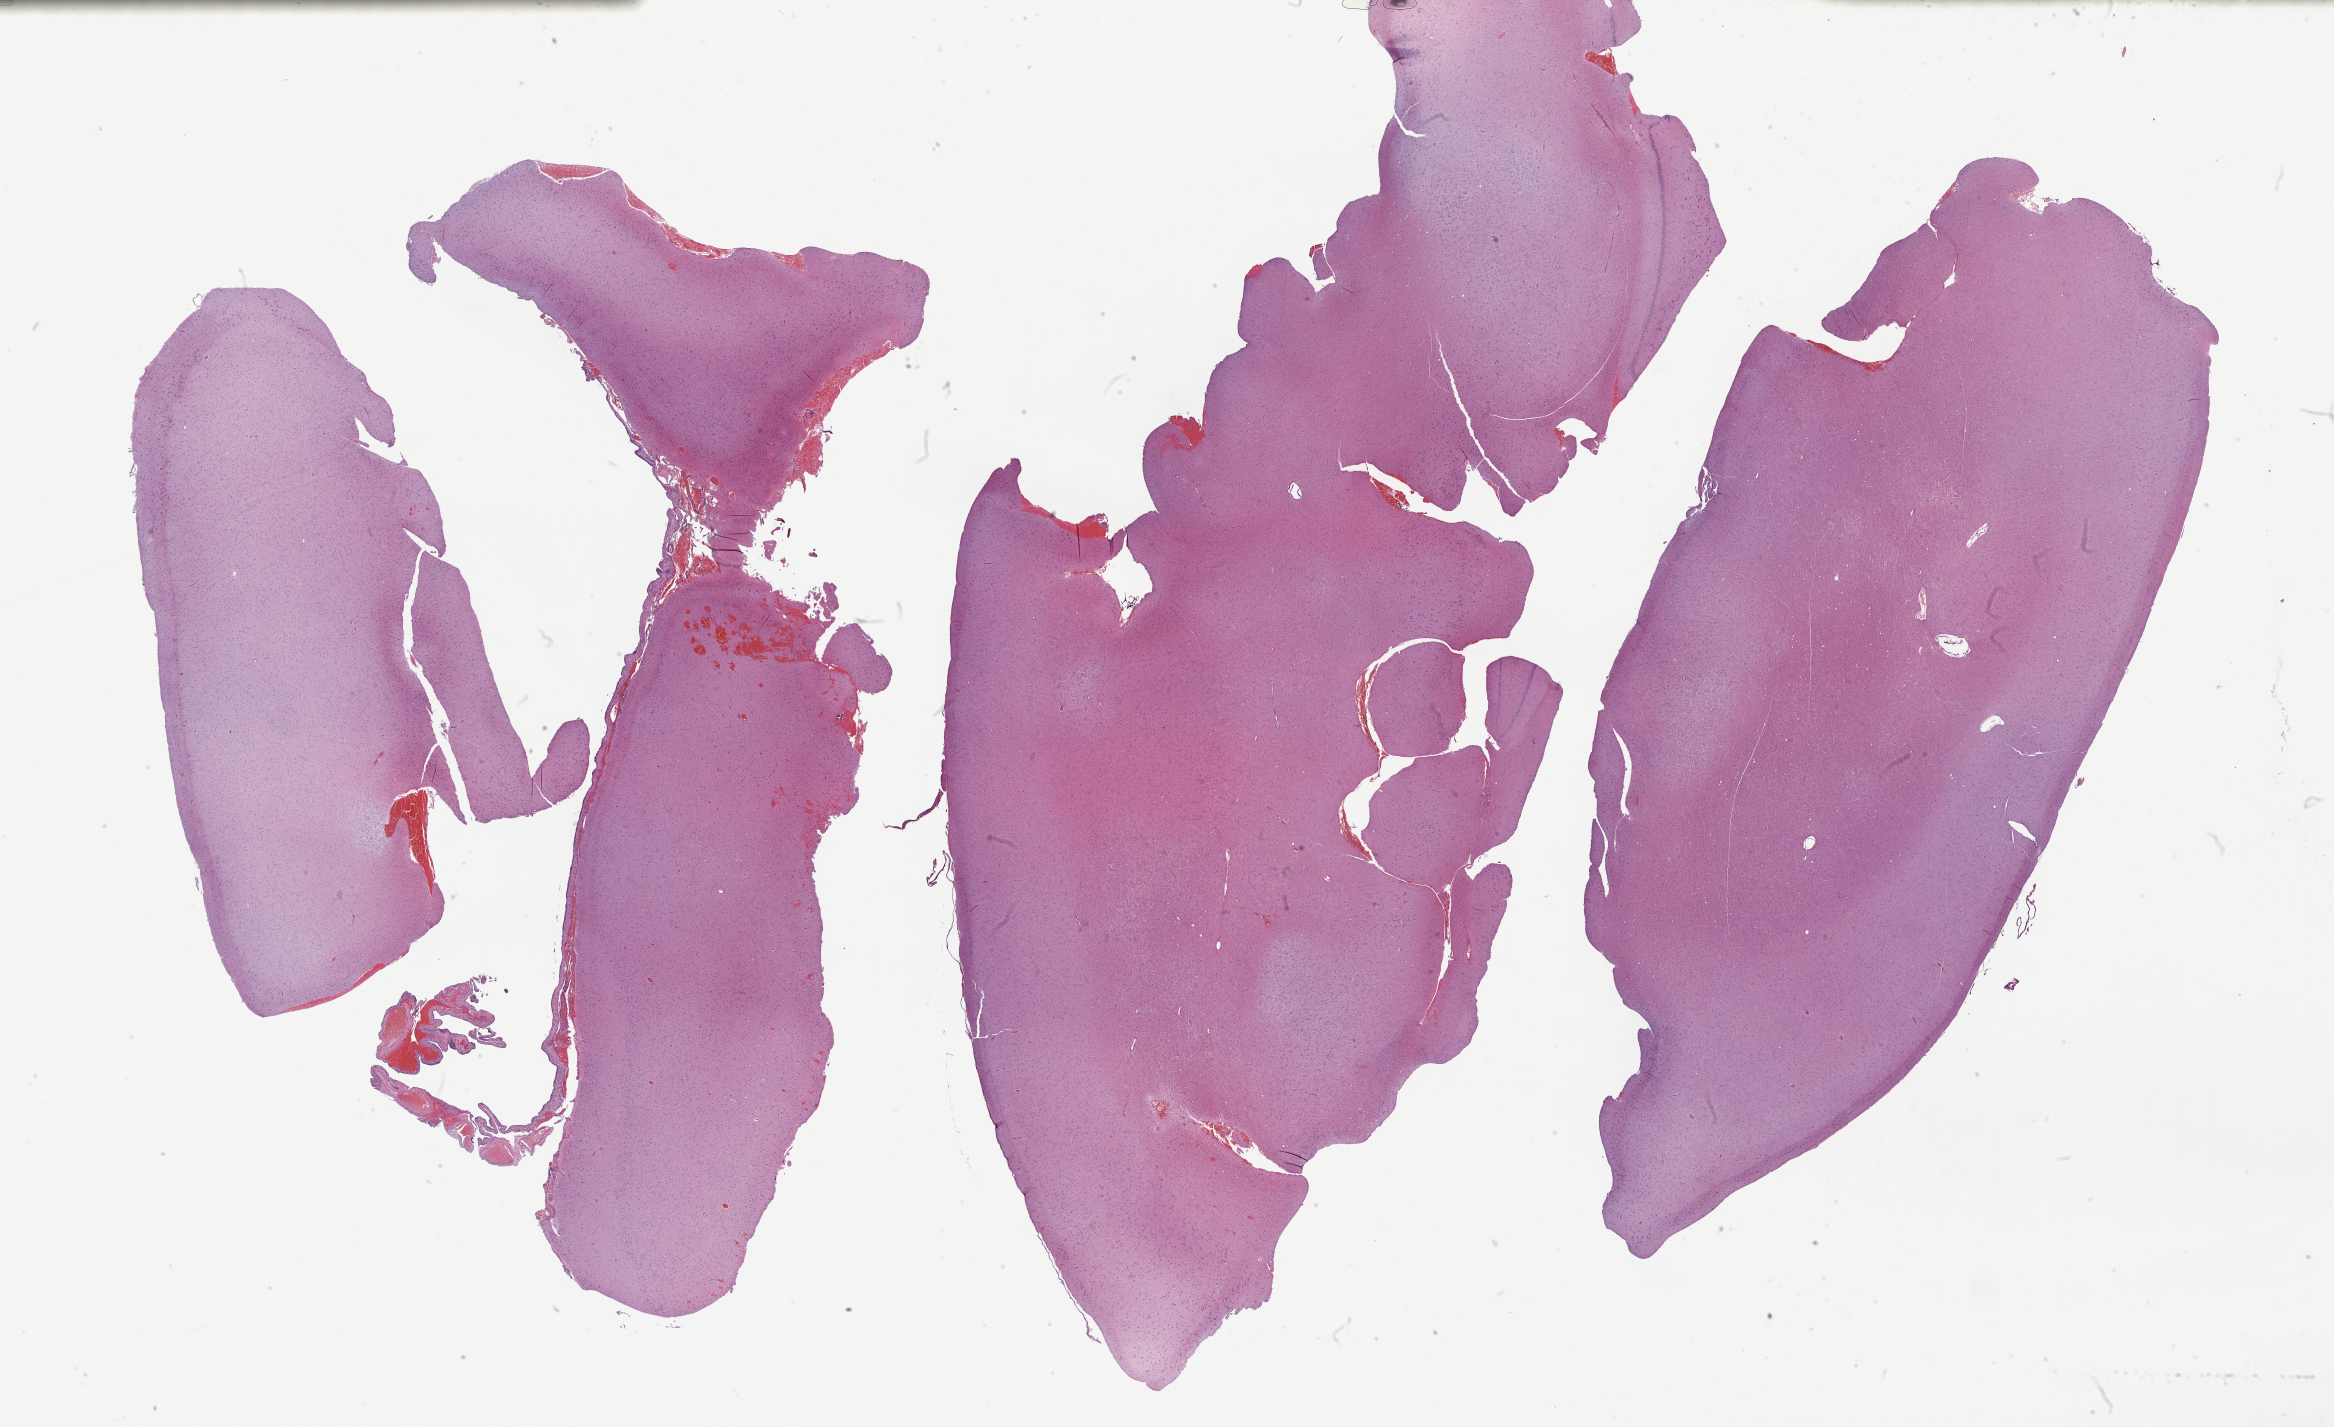
Hematoxylin and eosin (H&E) stained whole-slide image, low-resolution overview of the scanned area, about 37.8 x 23.1 mm; FFPE section; brain, primary tumour sample. Female patient; age at initial diagnosis 37 years. Histologic grade: G2 (moderately differentiated).
Laterality: left. Pathologic diagnosis: Astrocytoma, NOS (cerebrum).